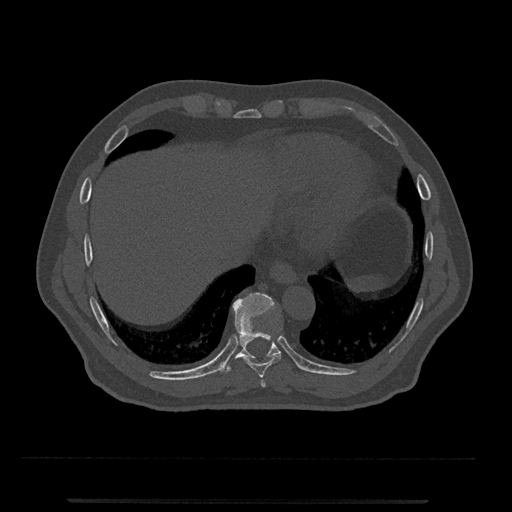
CT including the spine, one axial slice; slice 547 of 797 in the series (ordered by position); reconstruction kernel Br40s/3; bone window (W 1800 / L 400 HU); 512 × 512 image matrix. Patient: male, 63 years. Case-level facts recorded for this patient, not image findings: primary cancer: prostate.
Structures marked on this image (semi-automatically segmented with operator editing):
- T10 vertebra: bounding box (x1, y1, x2, y2) in pixels: (218, 293, 281, 374)
- T8 vertebra: (260, 379, 266, 387)
- T9 vertebra: (244, 329, 282, 378)